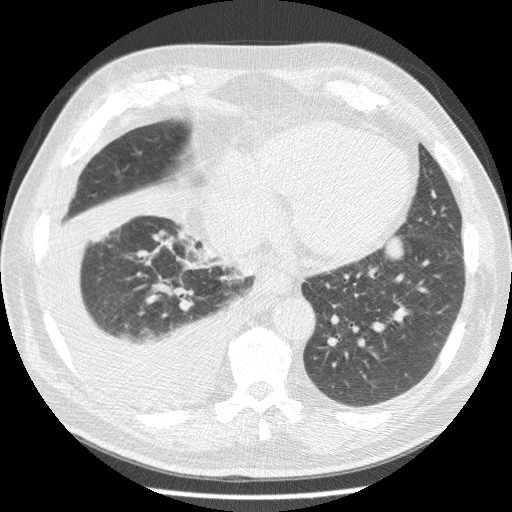
Chest CT (low-dose screening protocol), one axial image, third screening round (two years after baseline), lung window (W 1500 / L -600 HU), 2.5 mm slice thickness, standard (soft-tissue) reconstruction kernel (STANDARD), slice 64 of 180 in the series, 512 × 512 image matrix. Male, age 63 years at enrolment.
- Lesion marked by an expert reader, bounding box [x1, y1, x2, y2] px = [347, 227, 416, 300].
- Screening reader's record for this exam (one nodule recorded; not confirmed to be the boxed lesion): non-calcified nodule or mass ≥4 mm, left lower lobe, 34 × 31 mm, smooth margins, soft tissue attenuation, pre-existing on the prior screen: yes; interval growth: yes.
- Official screen result: positive, other.
- Later outcome: lung cancer diagnosed 30 days after this screen — squamous cell carcinoma, NOS, left lower lobe, stage IB (AJCC 6th edition), 48 mm at pathology.